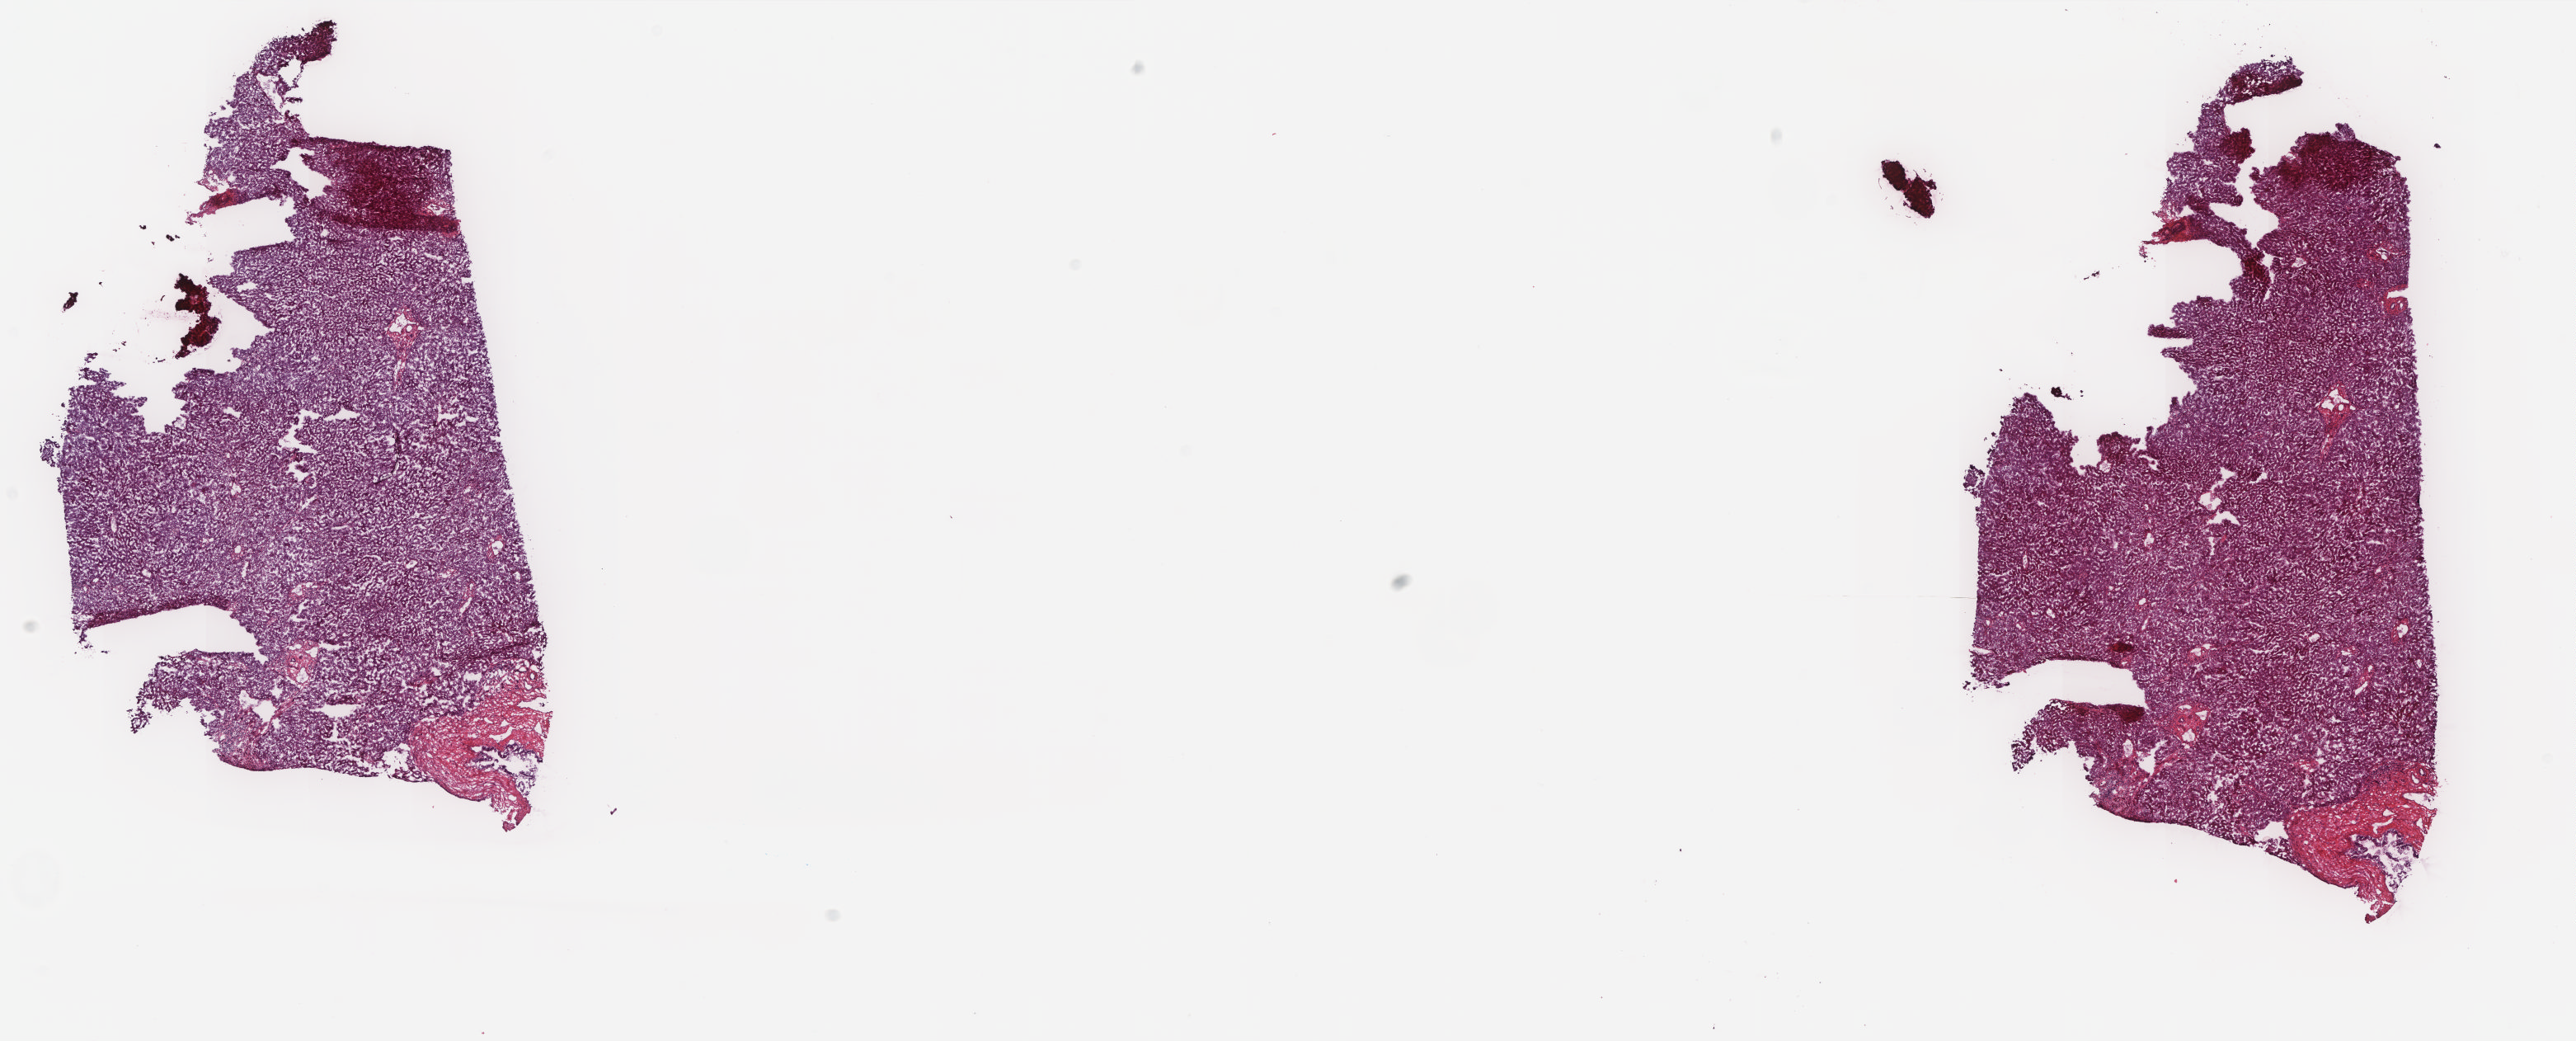
Digitized H&E tissue section (whole slide) — a low-resolution overview of the entire scanned area, about 25.0 x 10.1 mm, frozen section from the top of the tissue portion, solid tissue normal (non-tumour tissue) sample from the liver. Male, age 67 years at initial diagnosis.
This section: solid tissue normal (non-tumour) sample from the same patient. Patient diagnosis: Hepatocellular carcinoma, NOS.